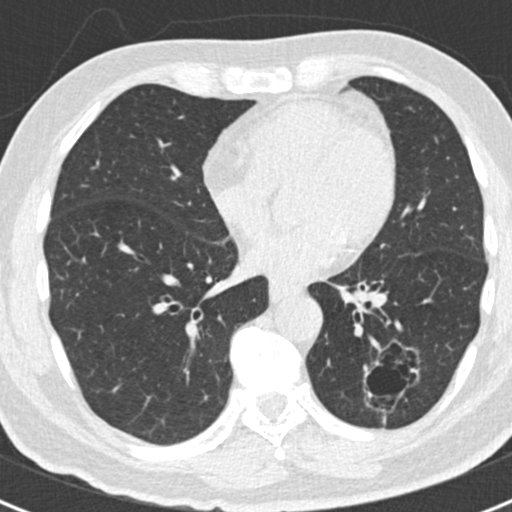
Axial slice from a low-dose chest CT screening exam, first (baseline) screen, lung window (W 1500 / L -600 HU), 2 mm slice thickness, standard (soft-tissue) reconstruction kernel (B30f). Male, age 66 years at enrolment. Former smoker at enrolment.
- Lesion marked by an expert reader, bounding box (x1, y1, x2, y2) in pixels: (343, 339, 420, 417).
- Screening reader's record for this exam (one nodule recorded; not confirmed to be the boxed lesion): non-calcified nodule or mass ≥4 mm, left lower lobe, 43 × 27 mm, smooth margins.
- Official screen result: positive, change unspecified: nodule(s) >= 4 mm or enlarging nodule(s), mass(es), or other non-specific abnormalities suspicious for lung cancer.
- Participant outcome: lung cancer diagnosed 801 days after this screen (after the third annual screen) — adenocarcinoma, NOS, left lower lobe, poorly differentiated (G3), stage IB (AJCC 6th edition), 38 mm at pathology.